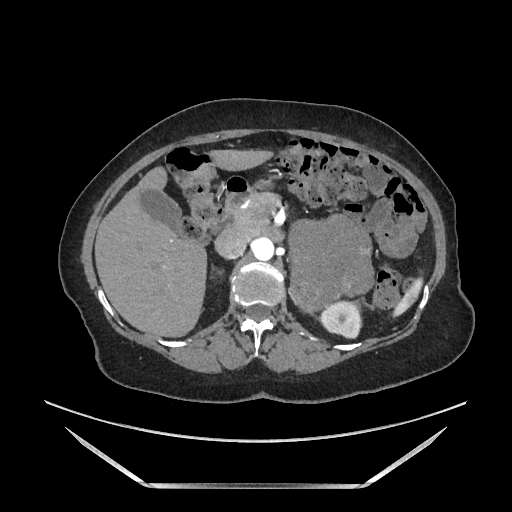
Contrast-enhanced abdominal CT, one axial slice. Position 102 of 205 along the scan axis. Soft-tissue window (W 400 / L 40 HU). 1.25 mm slice thickness. 512 × 512 image matrix, field of view 440 × 440 mm. Female patient. Case-level facts recorded for this patient, not image findings: diagnosis: adrenocortical carcinoma; tumour side: left adrenal; tumour size at pathology: 12.5 cm; Ki-67 index: 39 %.
Annotated regions visible in this slice (semi-automatically segmented with operator editing):
- mass: bounding box <291,217,372,310> (left, top, right, bottom; pixels)